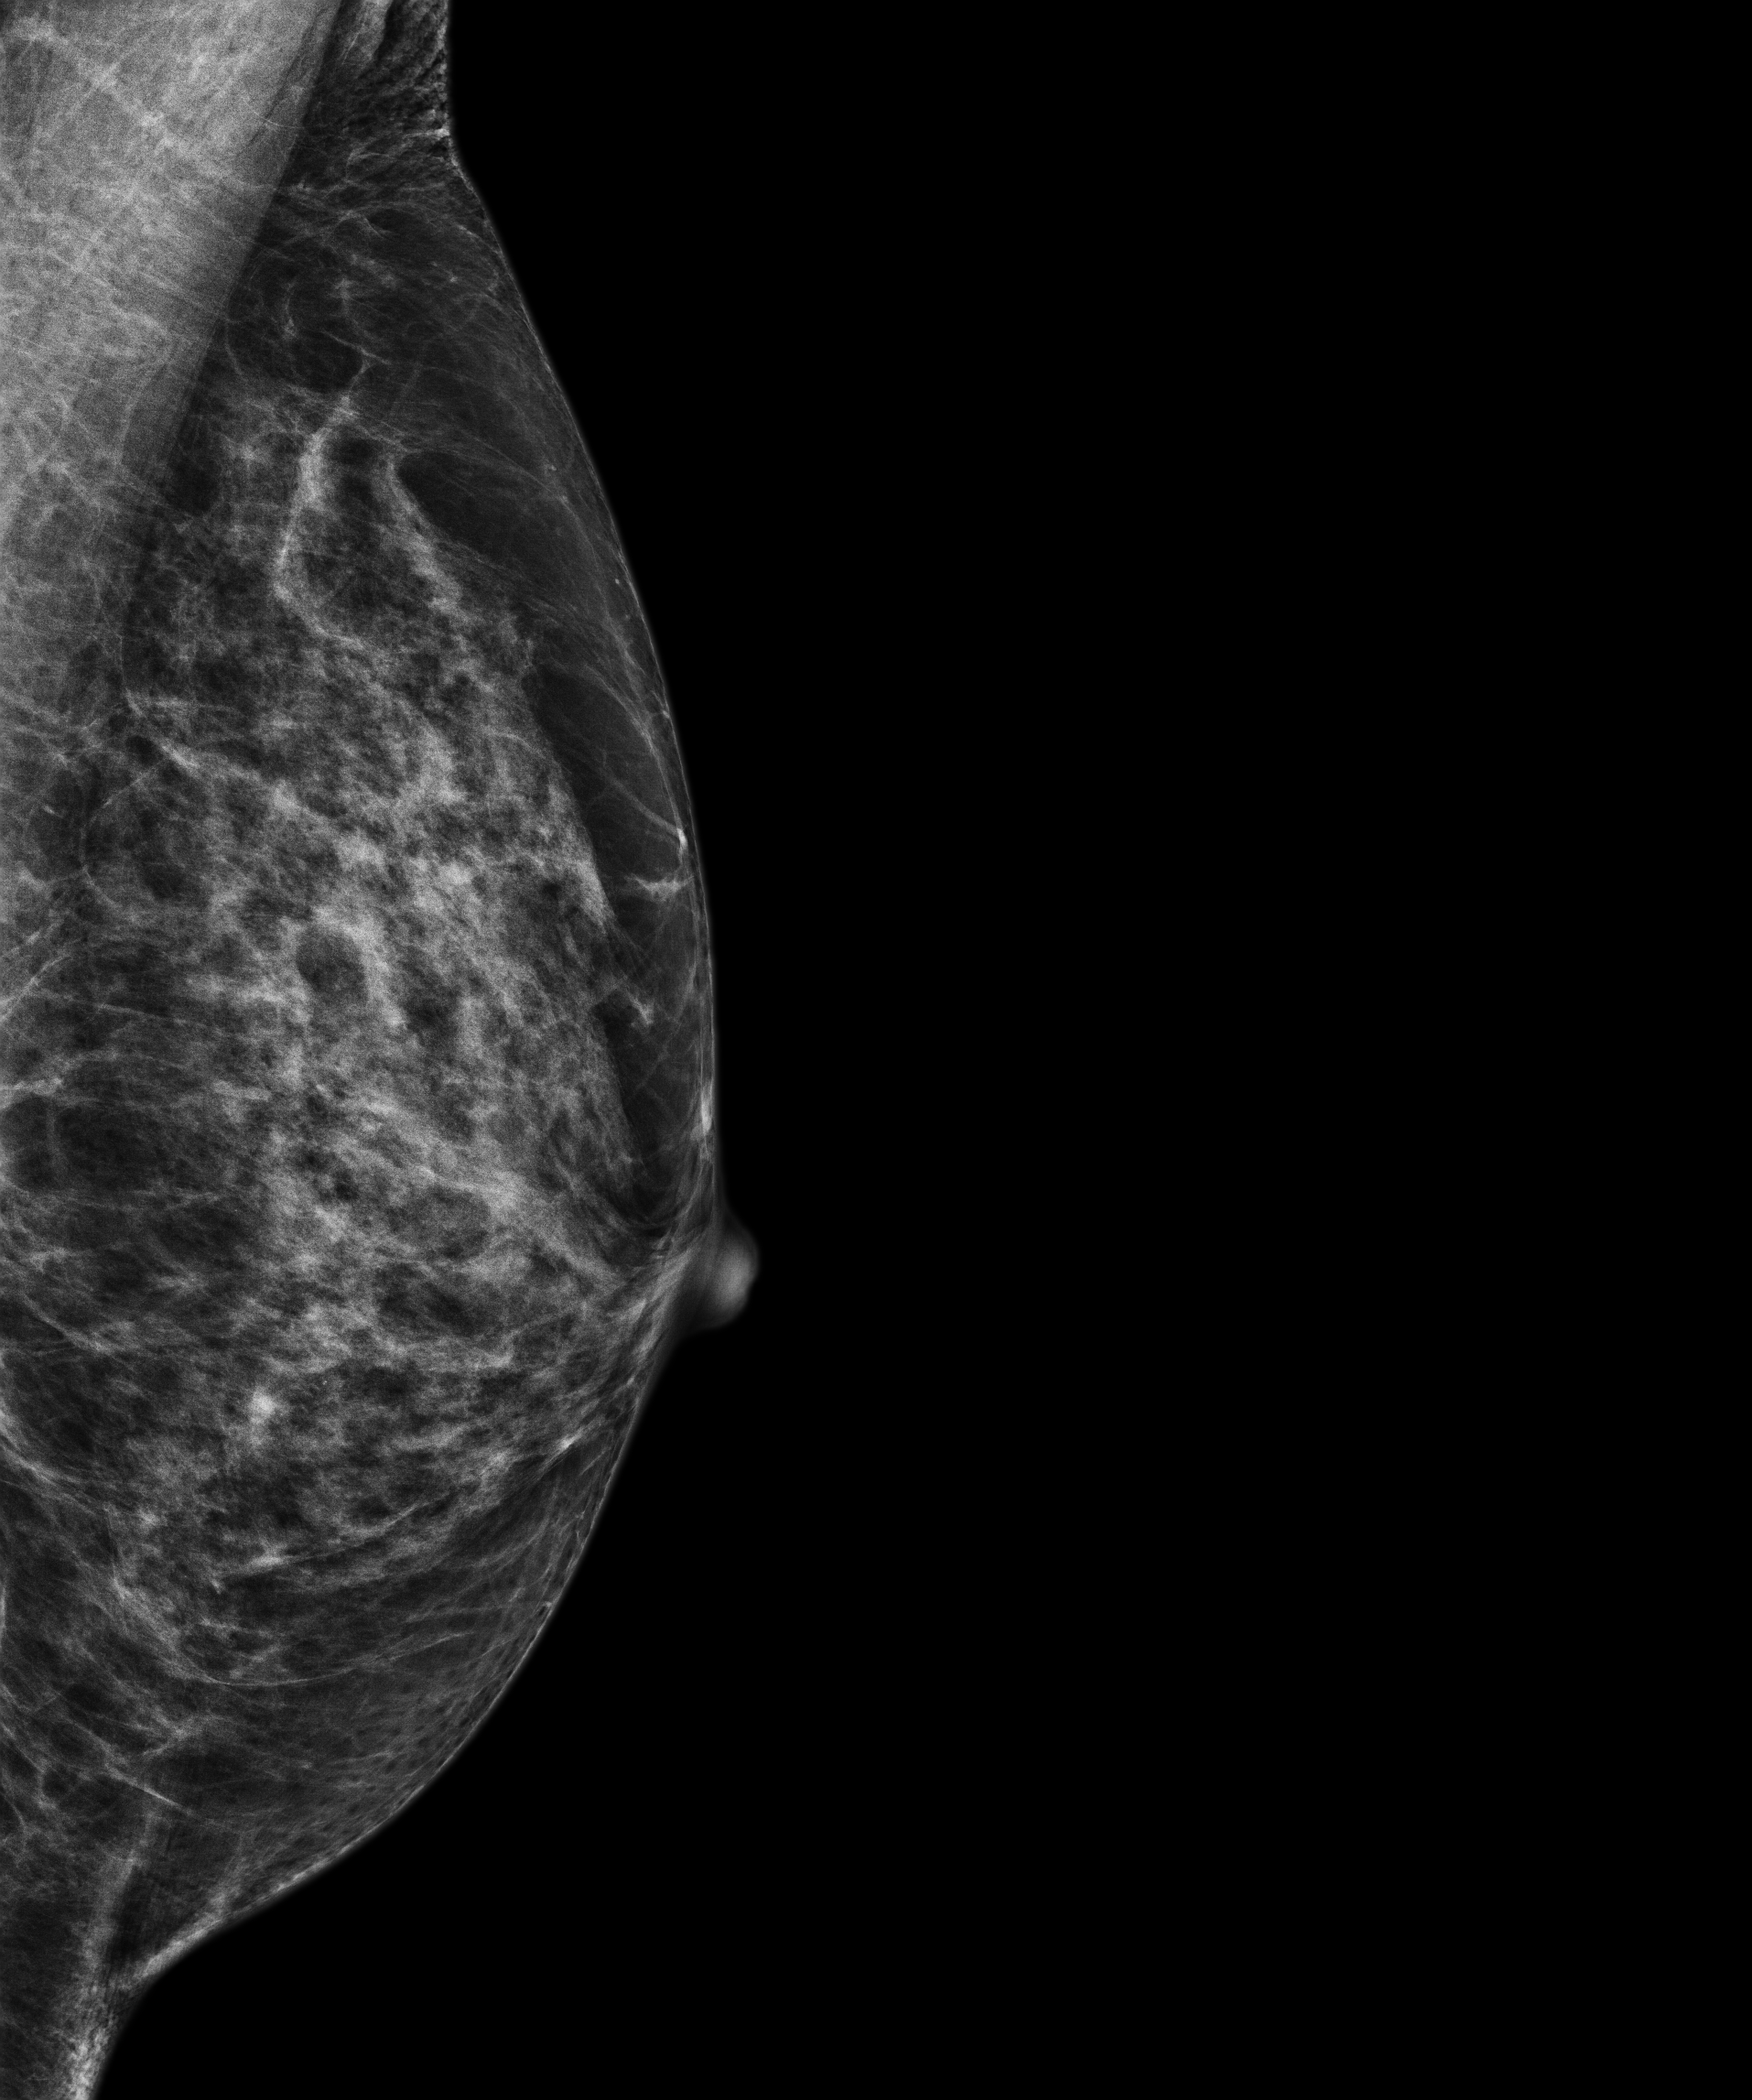
Screening examination. Patient aged 57 years (female).
Image type: full-field digital mammogram. Breast: left. Projection: MLO view.